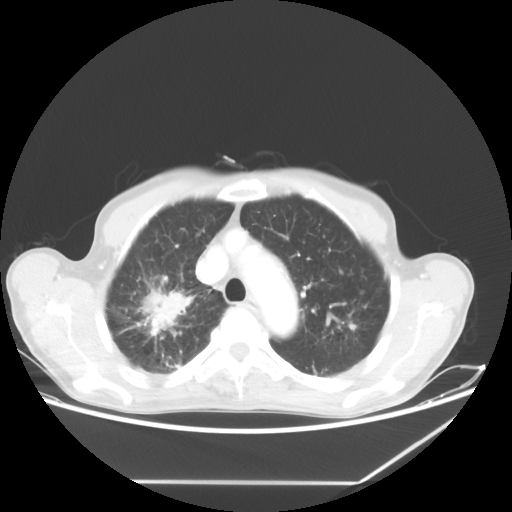
Chest CT, one axial slice. Position 49 of 65 along the scan axis. 80 kVp. Lung window (W 1500 / L -600 HU). 5 mm slice thickness. 512 × 512 image matrix. Male patient, age 68 years. Case-level facts recorded for this patient, not image findings: clinical TNM (as recorded): T3 N3 M0.
Annotated regions visible in this slice (rectangle marked by the reading radiologist):
- lung tumour (recorded histology: adenocarcinoma): bounding box [x1, y1, x2, y2] px = [130, 269, 189, 336]